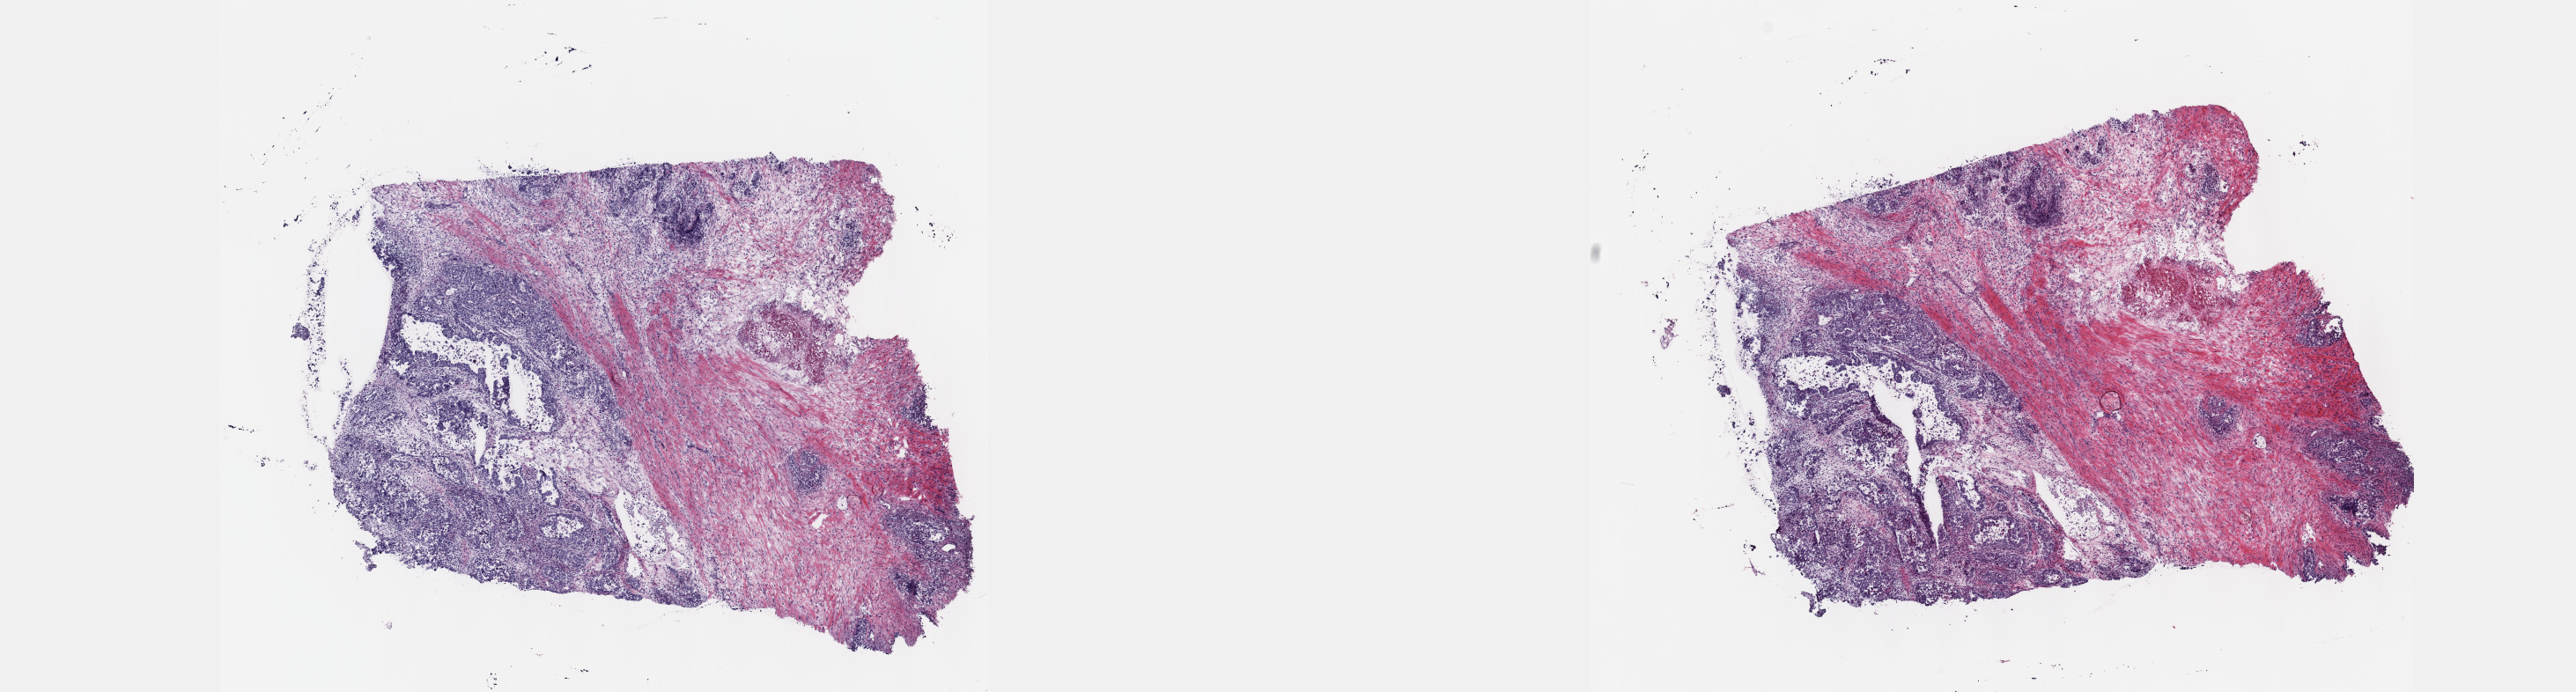
H&E whole-slide image, whole scanned area (about 23.6 x 6.4 mm) shown as a low-resolution overview, frozen section from the top of the tissue portion, sample: primary tumour, testis. Male patient; age at initial diagnosis 14 years. Pathologist review of this section (percent, as recorded): tumour cells 60%, tumour nuclei 60%, normal cells 10%, stromal cells 30%, necrosis 0%. Inflammatory infiltration, as recorded: lymphocyte infiltration 40%, monocyte infiltration 20%, neutrophil infiltration 20%.
• pathologic diagnosis: Mixed germ cell tumor
• AJCC pathologic stage: II